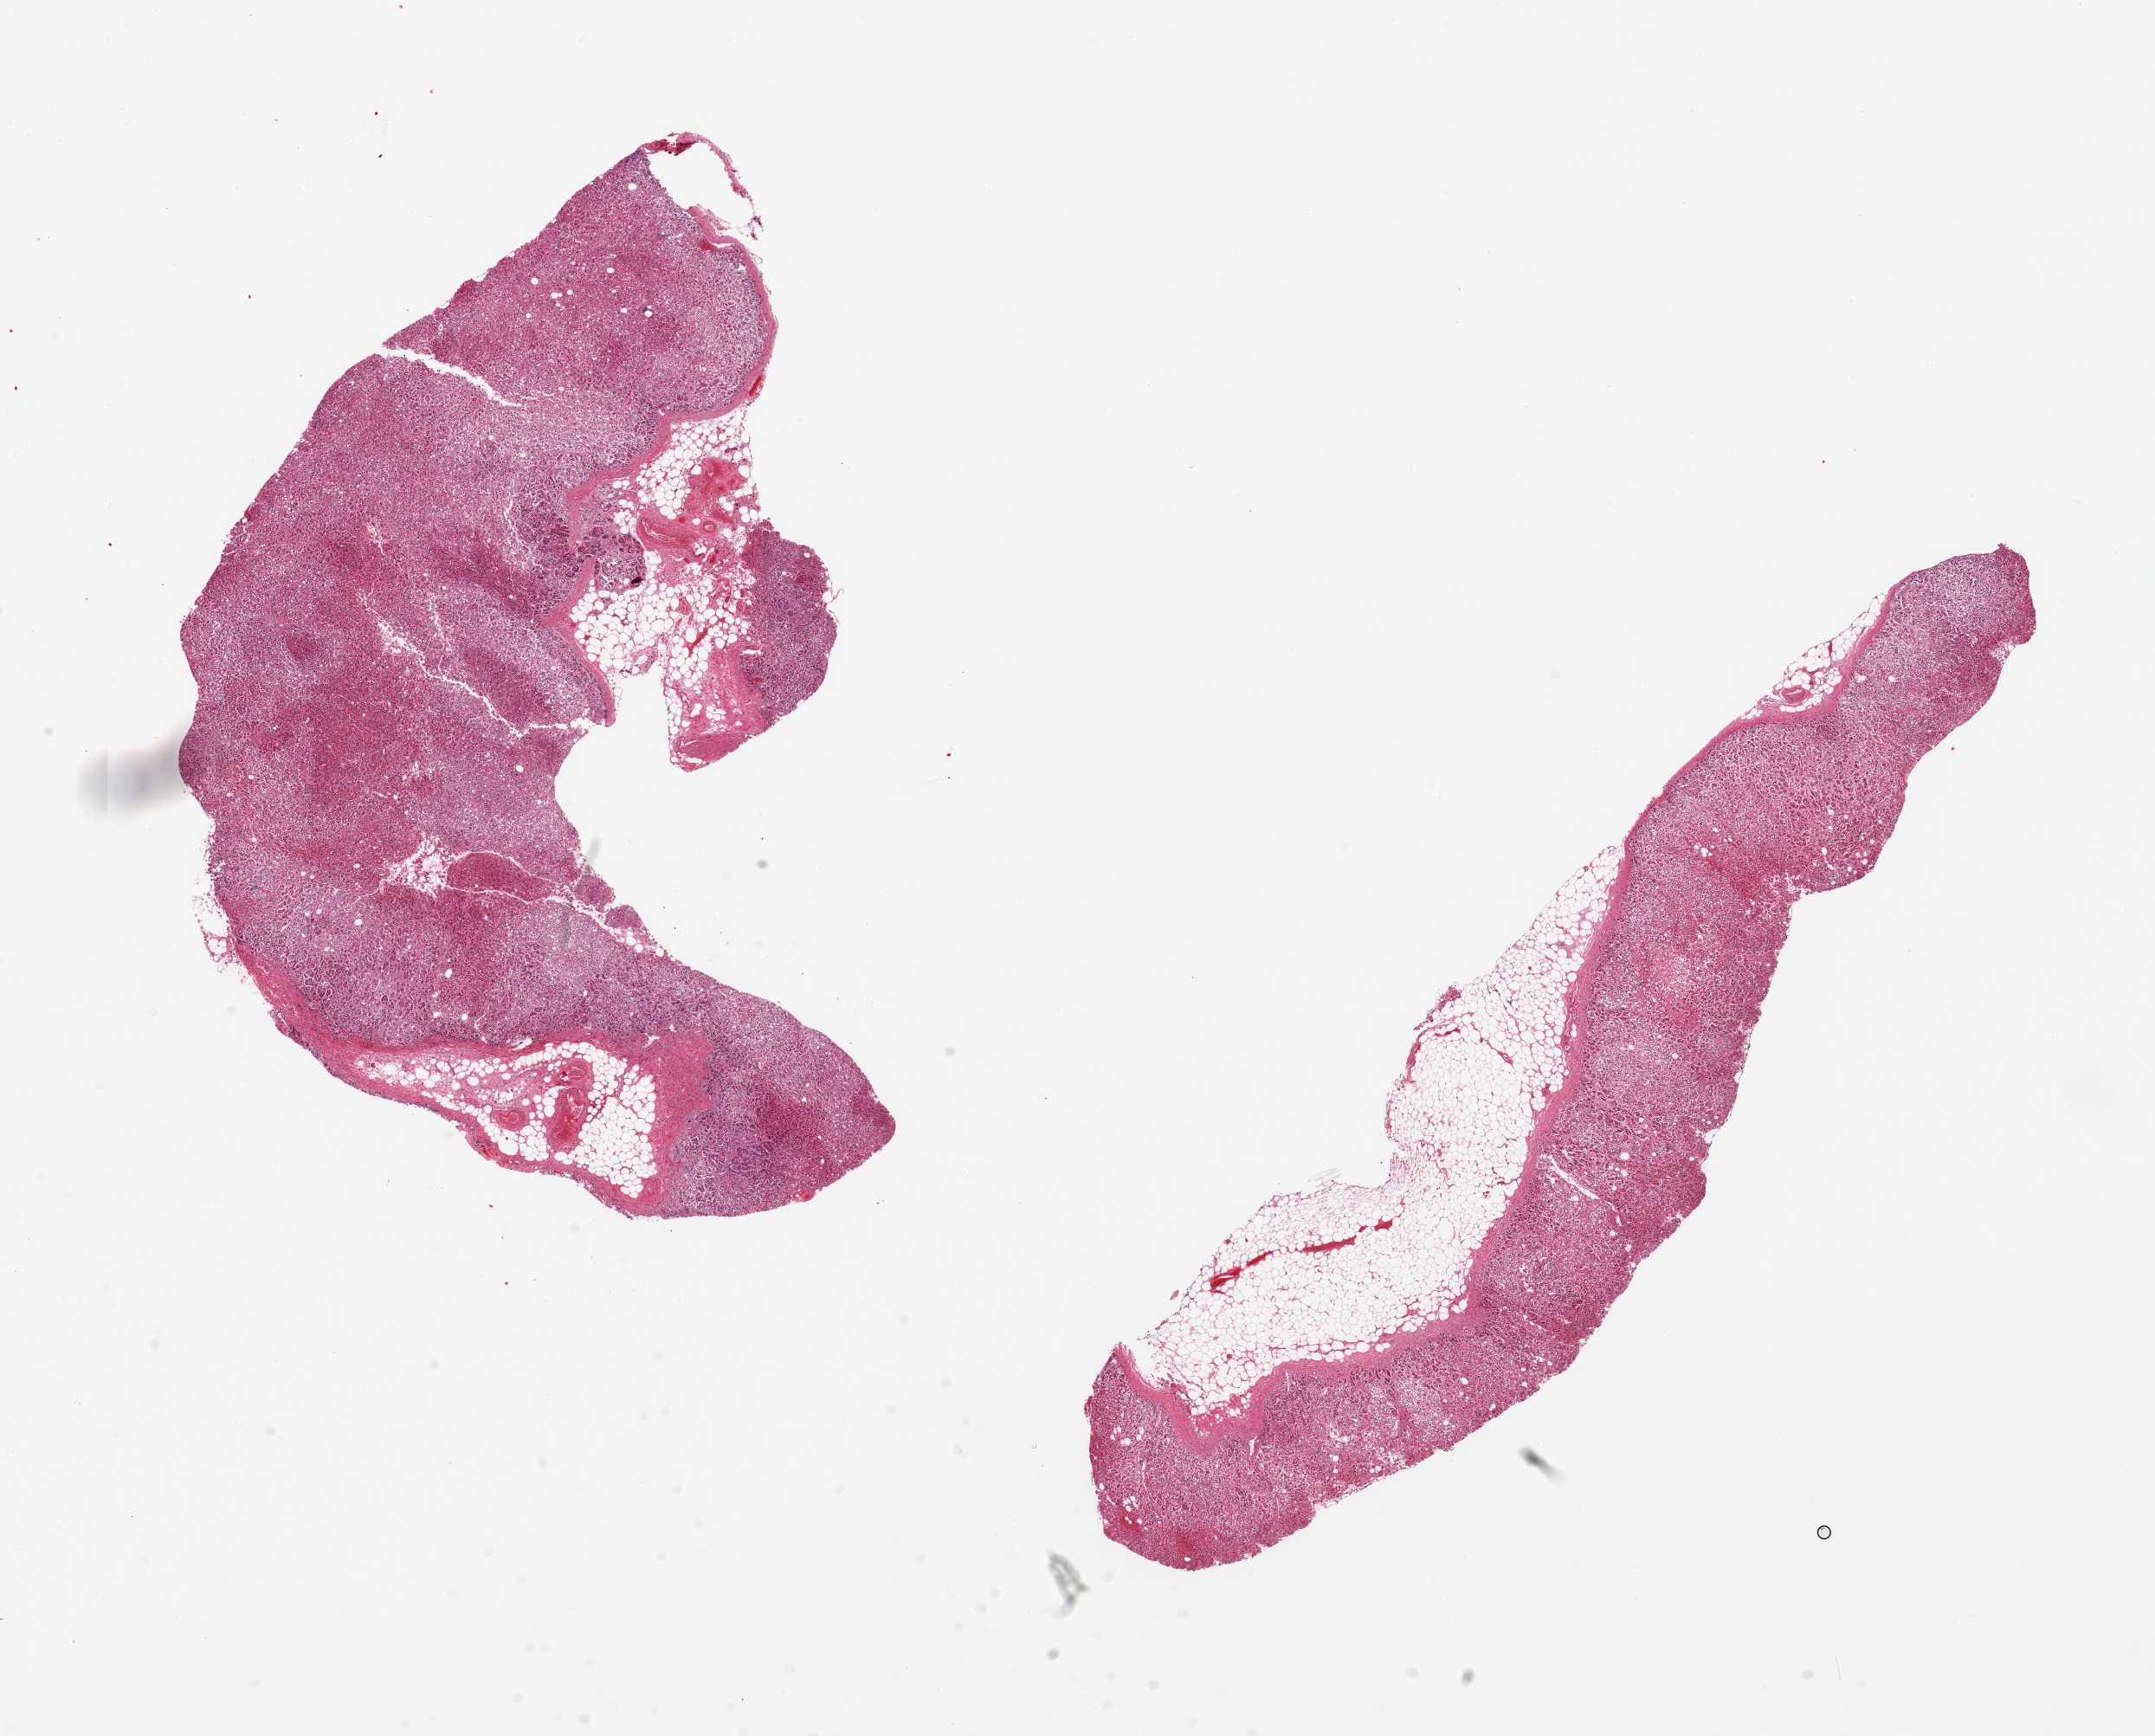
Digitized hematoxylin and eosin (H&E)-stained section, brightfield, low-resolution overview of the scanned area, about 19.7 x 15.9 mm, PAXgene-fixed, paraffin-embedded tissue, section of adrenal gland (target tissue), donor tissue sample. Donor sex: male.
Reviewer comment on this tissue sample: 2 aliquots, ~10x2mm, all cortex, badly autolyzed.